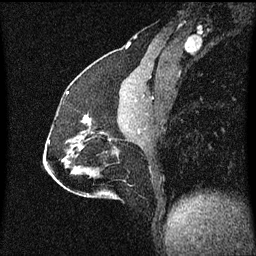
Breast MRI (dynamic contrast-enhanced), one sagittal slice. Position 28 of 60 along the scan axis. Dynamic contrast-enhanced series, image 2 of 3 at this slice position (ordered by acquisition). 1.5 T. TE 4.2 ms, TR 8.4 ms. 2 mm slice thickness. 256 × 256 image matrix. Patient: female, 51 years.
Structures marked on this image (semi-automatically segmented with operator editing):
- analysis volume of interest (the breast-tissue region the enhancement analysis was run in; not a lesion): box from (x=80, y=116) to (x=107, y=139) px
- tumour enhancement mask (voxels above the 70 % enhancement threshold inside the analysis volume of interest): (x=83, y=116)–(x=102, y=133)